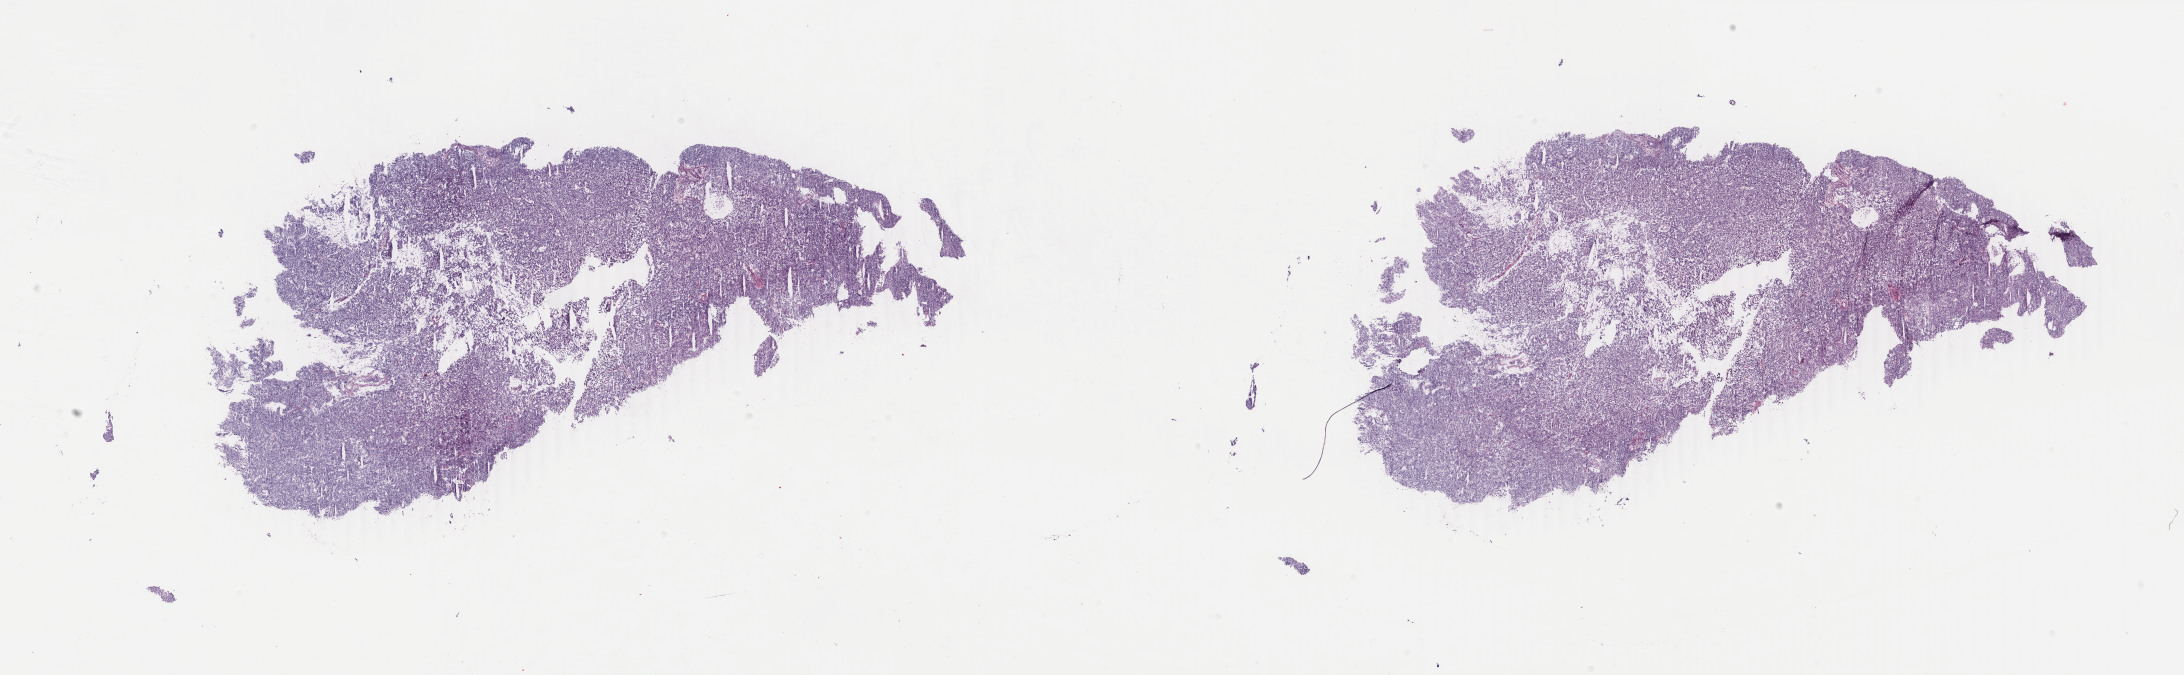
Whole-slide histology image, H&E-stained, low-resolution overview of the scanned area, about 34.7 x 10.7 mm; frozen section from the top of the tissue portion; sample: primary tumour, uterus. Patient: female, age at initial diagnosis 68 years.
Histologic diagnosis: Endometrioid adenocarcinoma, NOS.